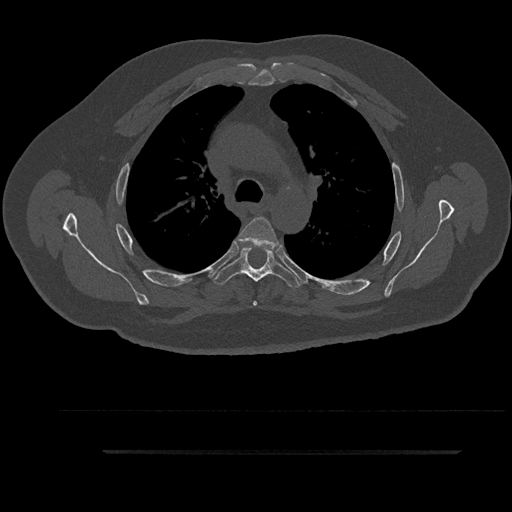
CT including the spine, one axial slice. Slice 645 of 797 in the series (ordered by position). Reconstruction kernel Br40s/3. Bone window (W 1800 / L 400 HU). 0.5 mm slice thickness. 512 × 512 image matrix, field of view 432 × 432 mm. Male patient, age 63 years. Case-level facts recorded for this patient, not image findings: primary cancer: renal; vertebrae with lytic lesions (as recorded): T8.
Structures marked on this image (semi-automatically segmented with operator editing):
- T4 vertebra: bounding box [x1, y1, x2, y2] px = [238, 217, 281, 306]
- T5 vertebra: [214, 246, 300, 290]